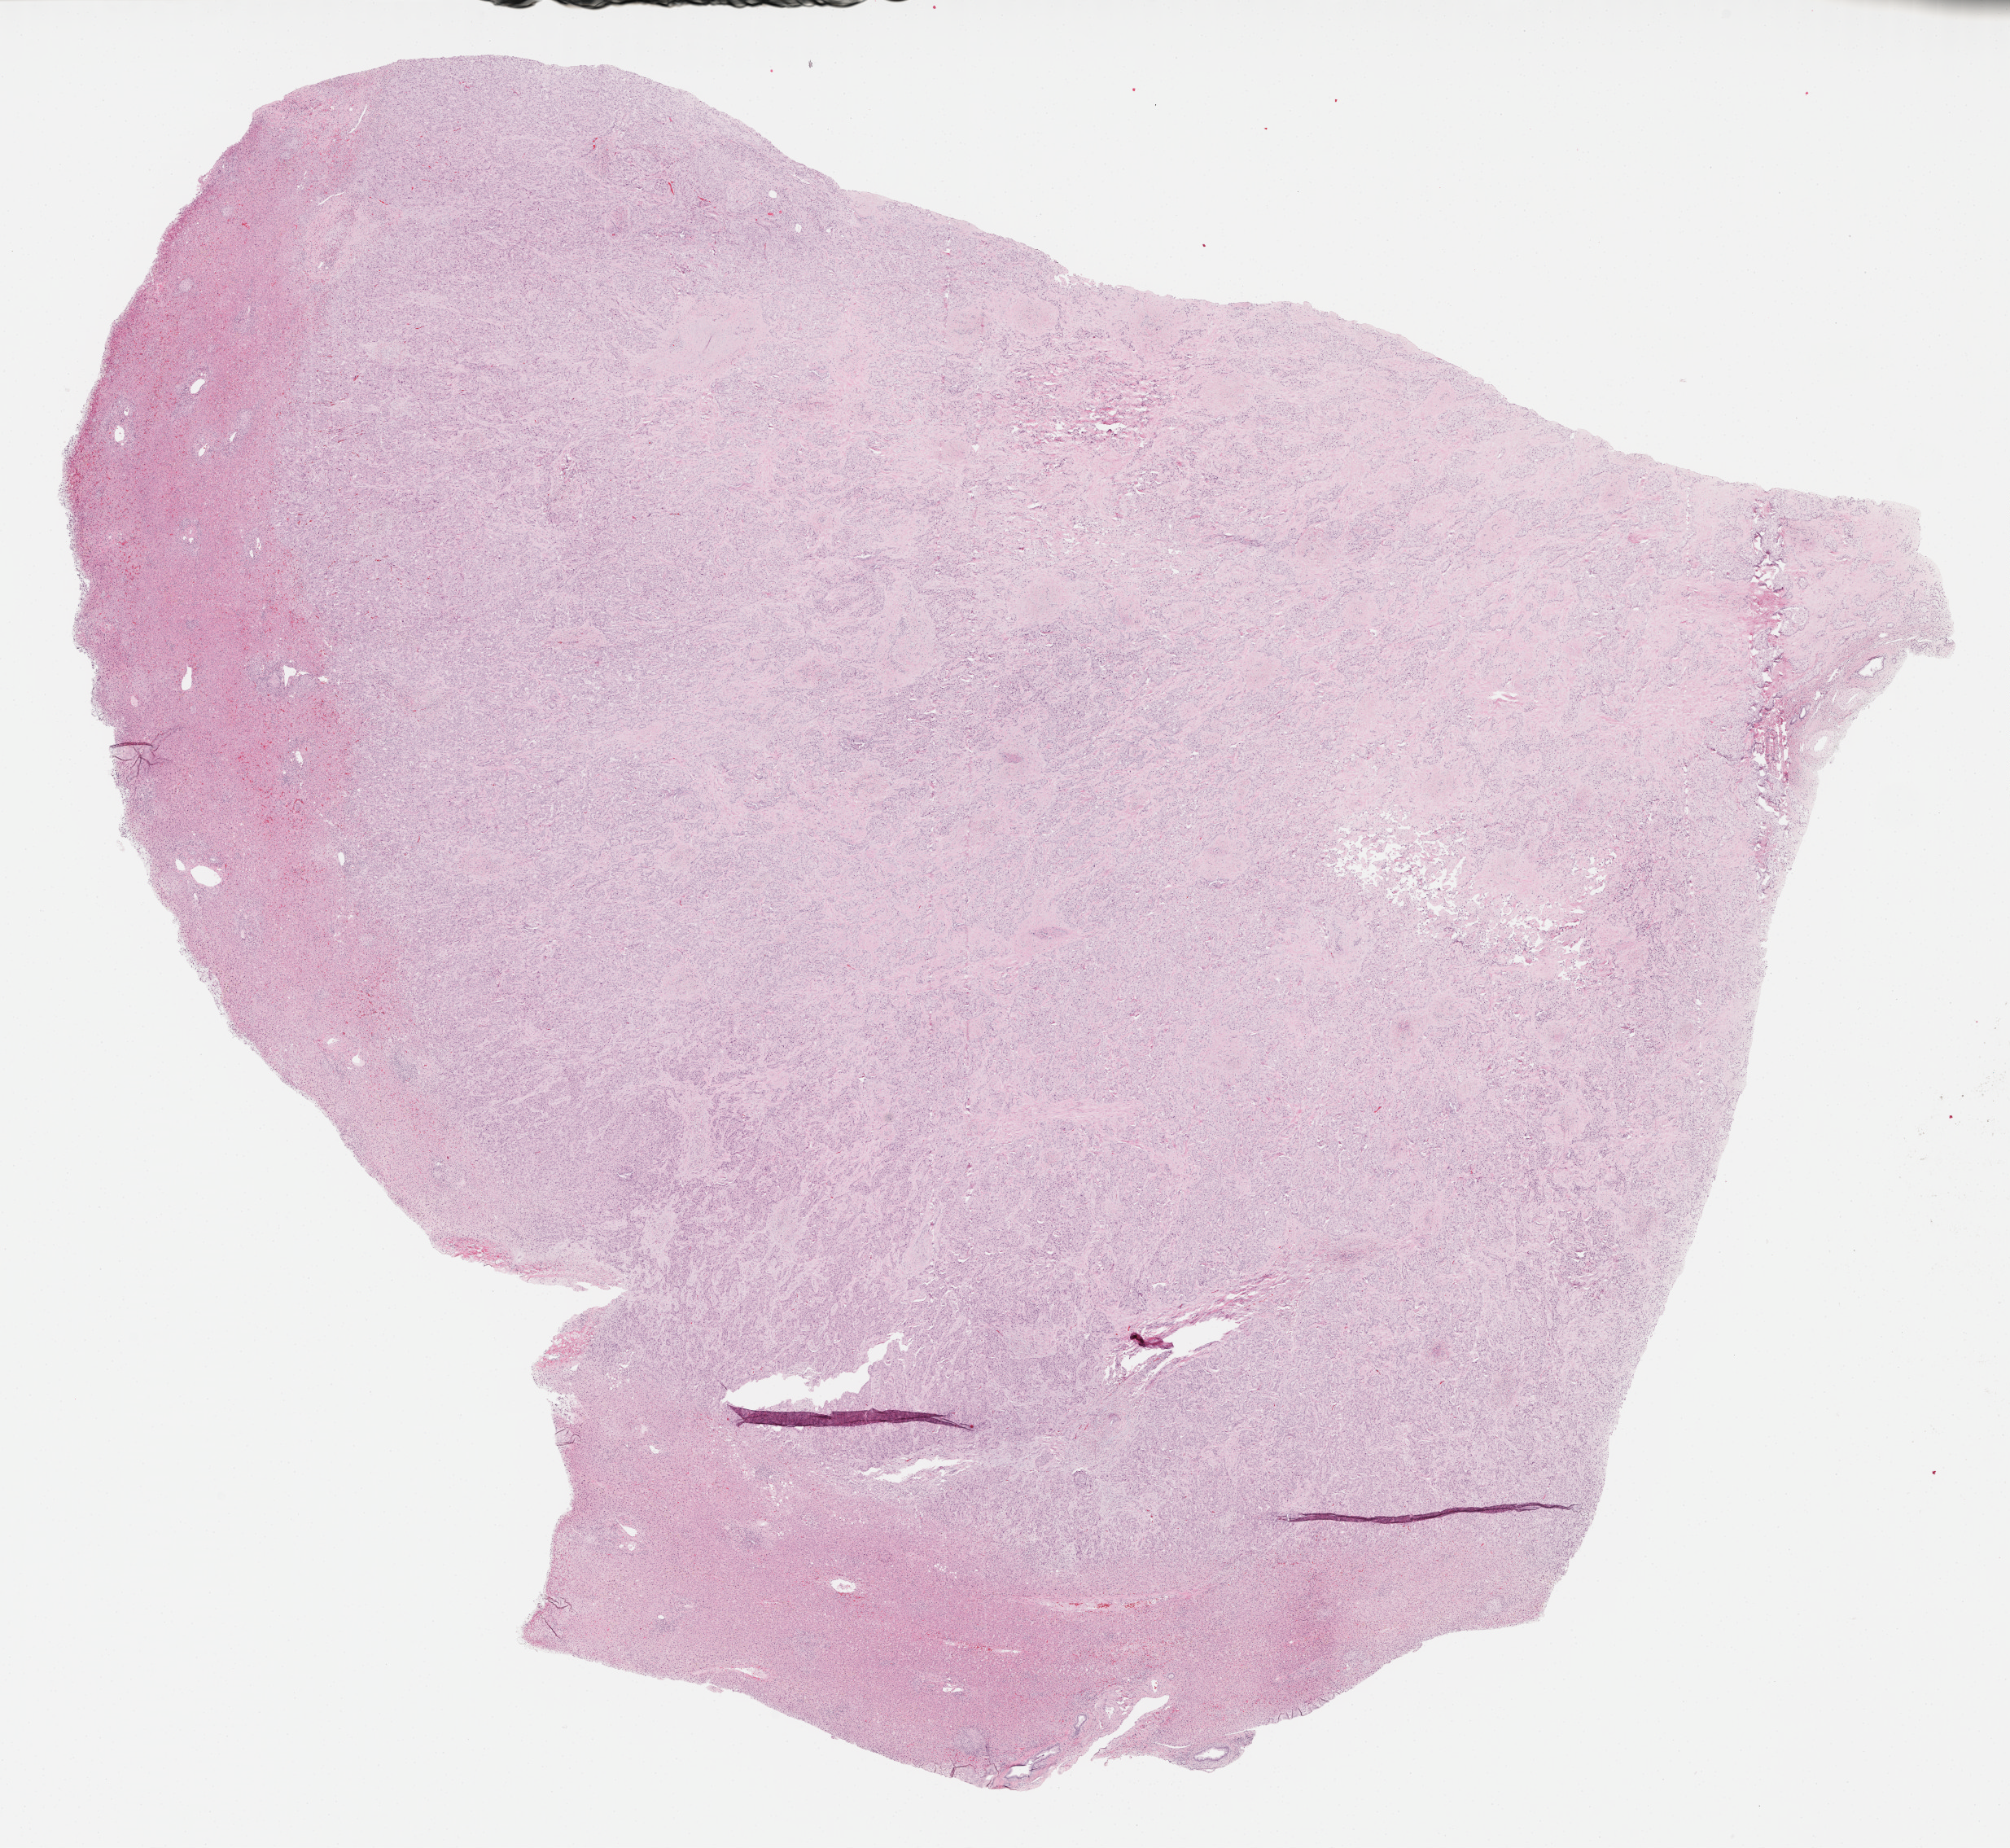
Digitized Hematoxylin and eosin (H&E) stained tissue section (whole slide), low-resolution overview of the scanned area, about 20.0 x 18.4 mm (from a 40x scan). FFPE section. Bile duct, primary tumour sample. Female, age 62 years at initial diagnosis. Histologic grade: G3 (poorly differentiated).
* diagnosis: Cholangiocarcinoma (intrahepatic bile duct)
* AJCC pathologic stage: I (7th edition)